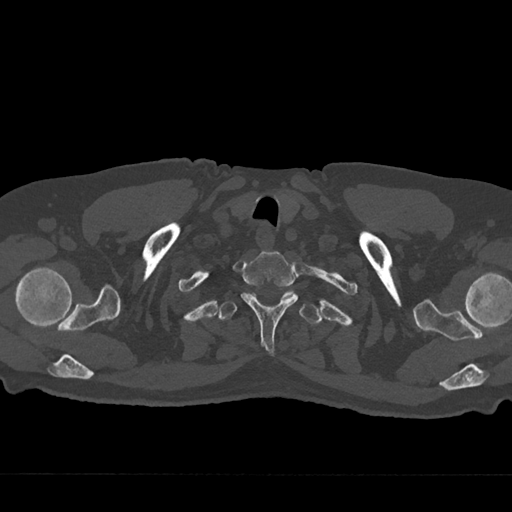
CT including the spine, one axial slice. Slice 647 of 797 in the series (ordered by position). Reconstruction kernel Br40s/3. Bone window (W 1800 / L 400 HU). 0.5 mm slice thickness. 512 × 512 image matrix. Patient: male, 75 years. From the clinical record (not read from this slice): primary cancer: renal.
Structures marked on this image (semi-automatically segmented with operator editing):
- T1 vertebra: bounding box <241,251,298,355> (left, top, right, bottom; pixels)
- T2 vertebra: <218,290,322,324>